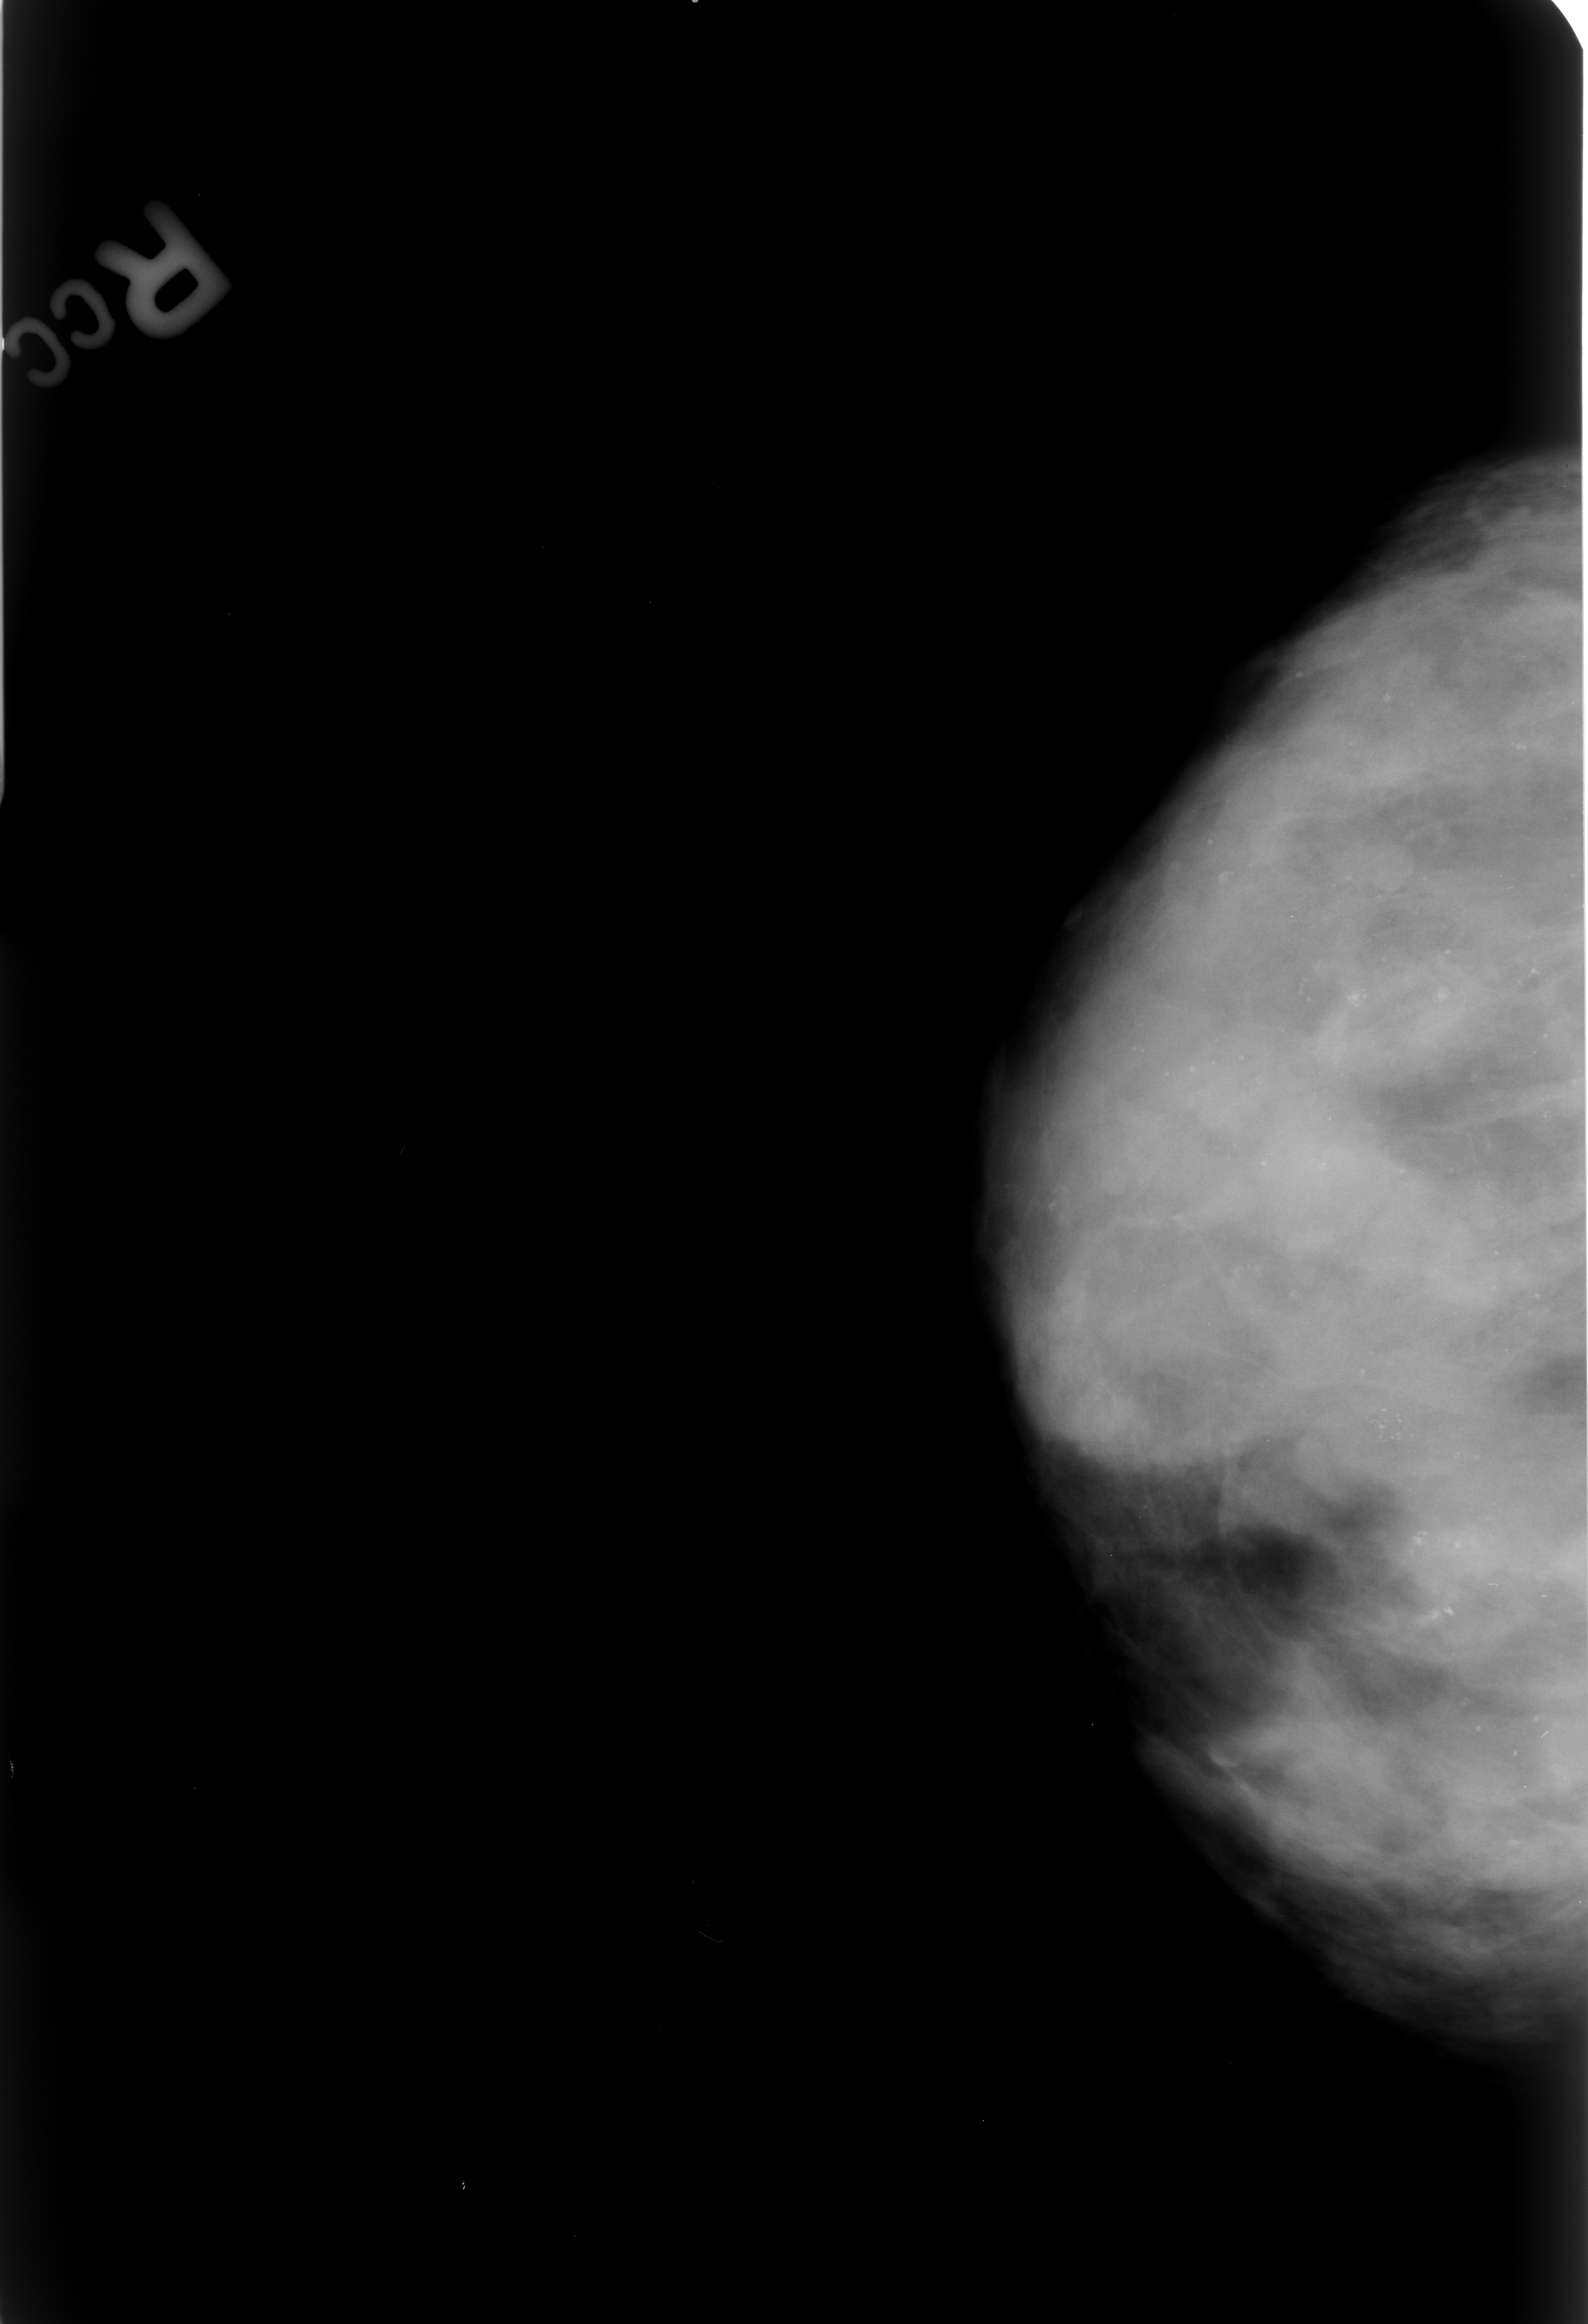
Digitized screen-film mammogram, right breast, craniocaudal (CC) view.
Radiologist-marked abnormalities on this image: calcifications, morphology punctate / pleomorphic, distribution clustered; BI-RADS assessment category 4; pathology (as recorded): benign.